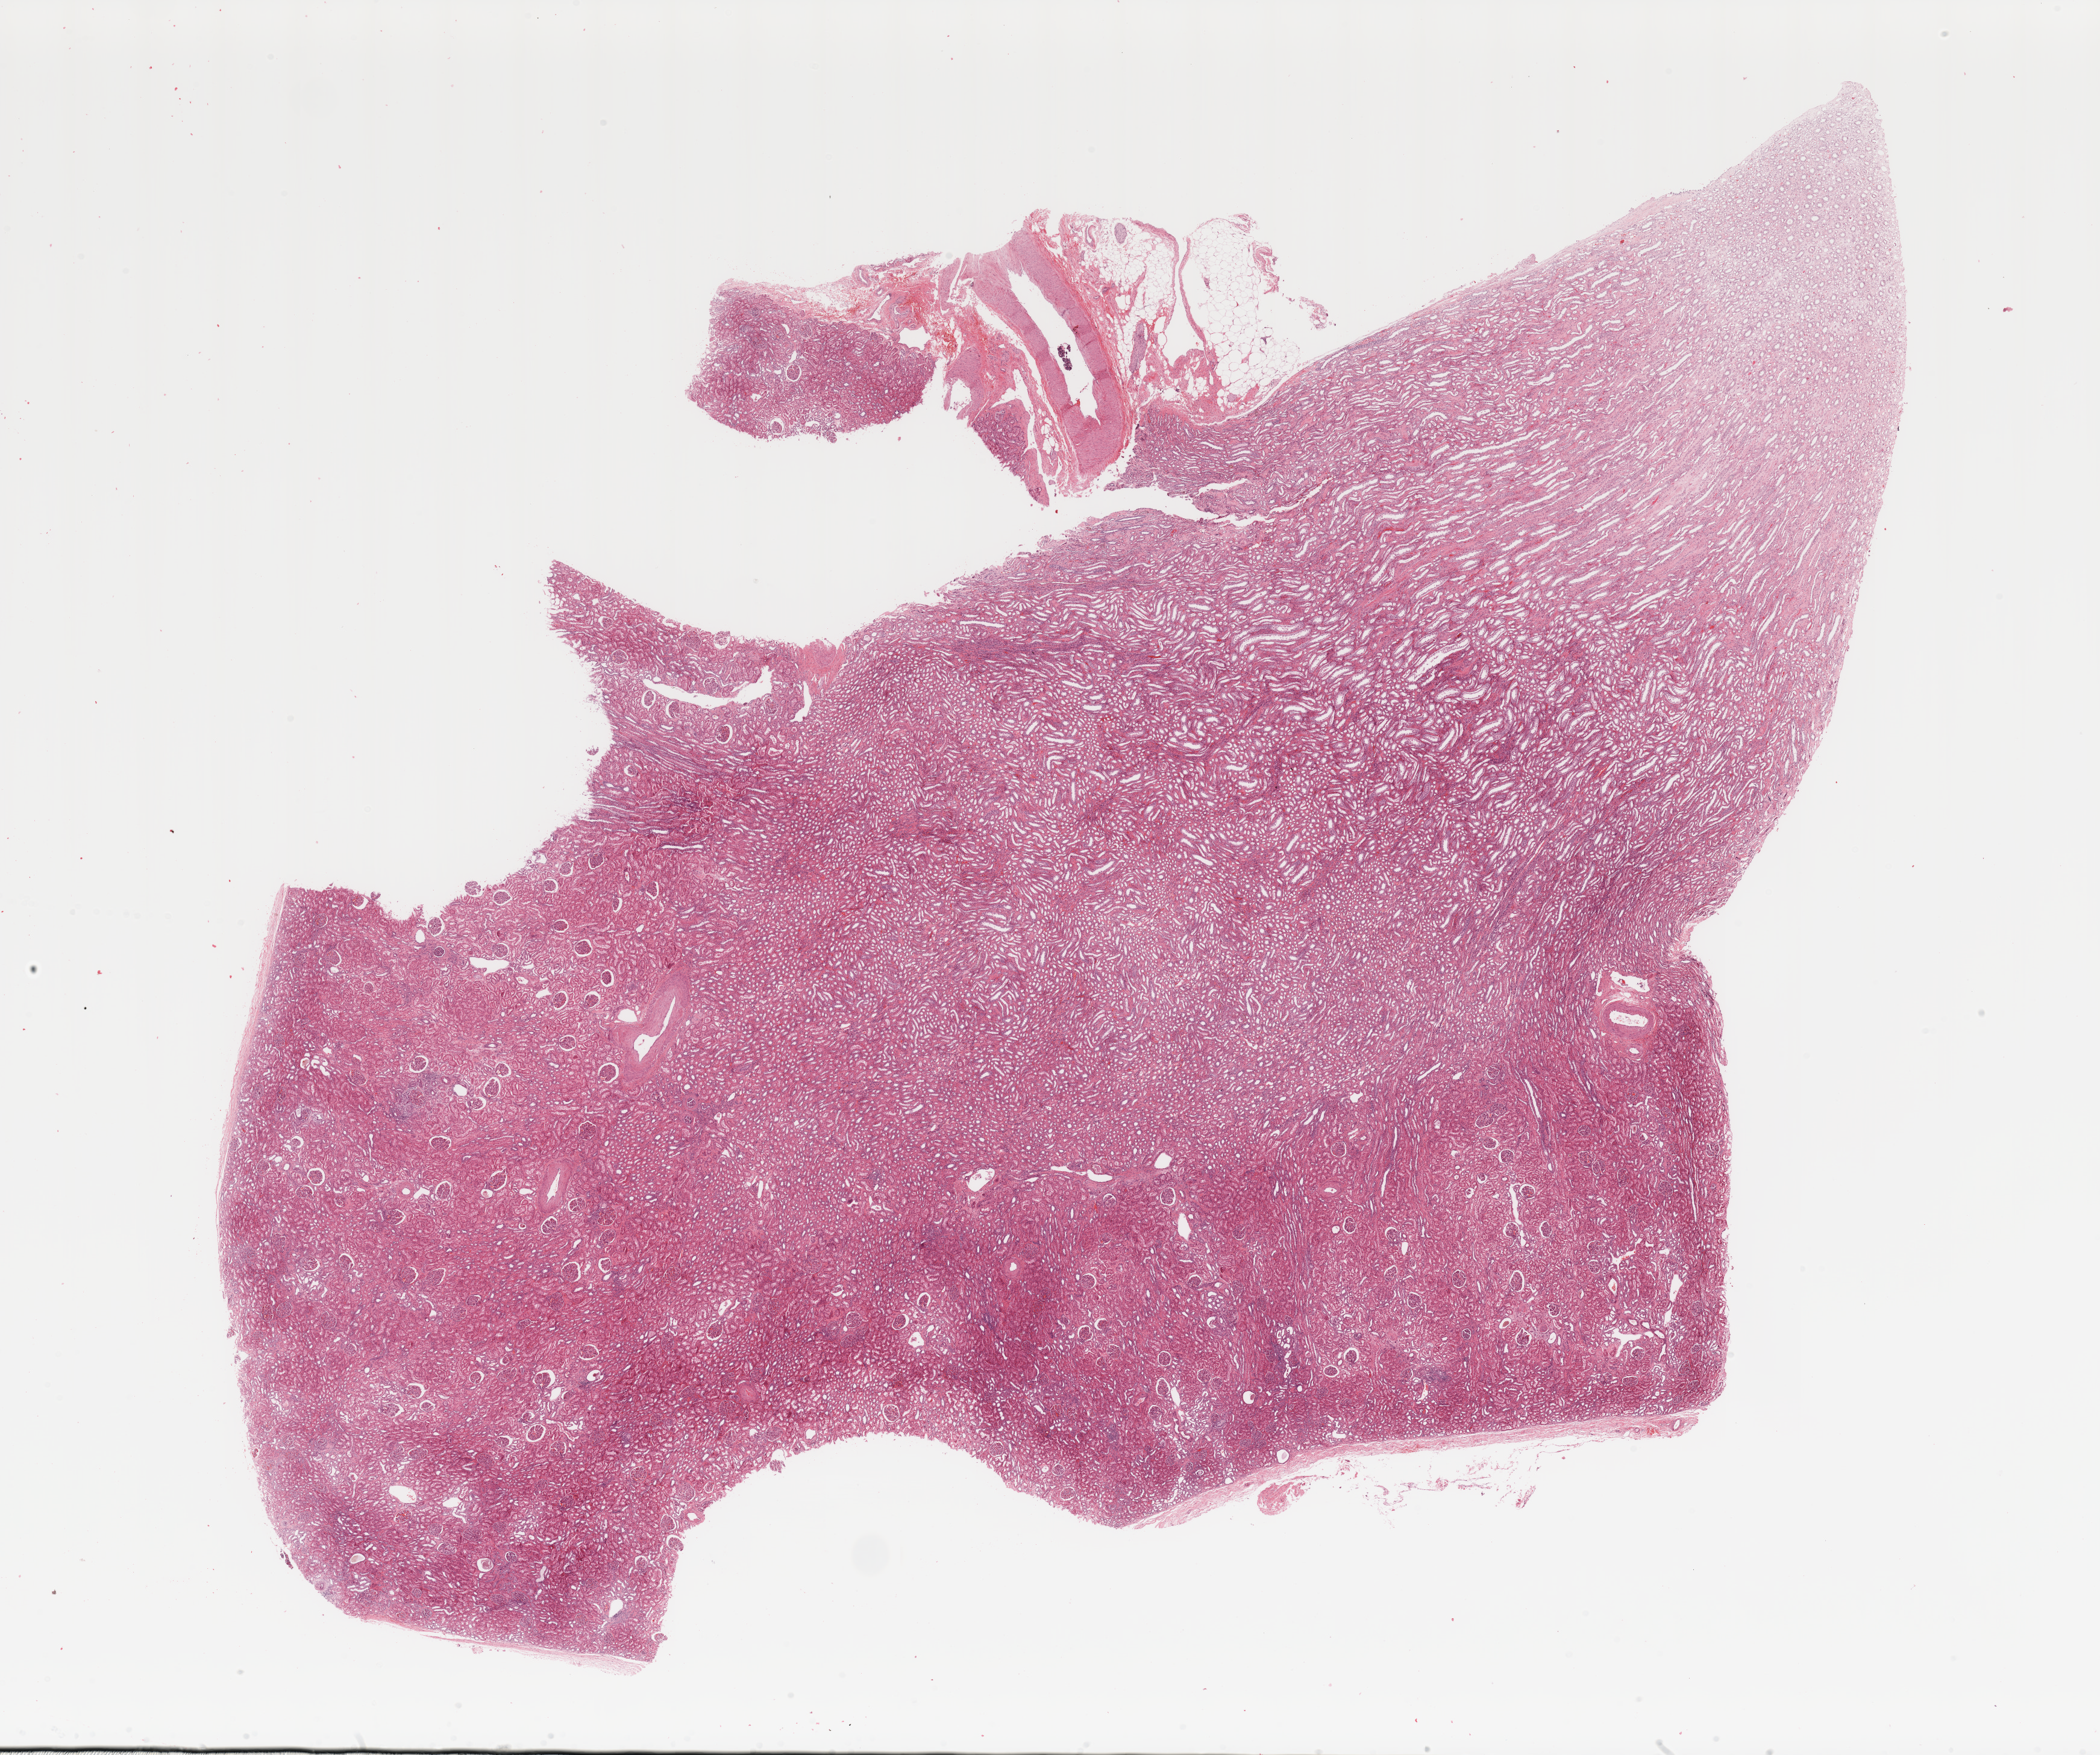
Whole-slide histology image, H&E-stained — whole scanned area (about 27.6 x 23.0 mm, acquisition: 20x scan) shown as a low-resolution overview, normal (non-tumour) tissue sample, sampled site: kidney. Patient: female, age 57 years.
This section: normal (non-tumour) tissue from the same patient. Patient diagnosis: Renal cell carcinoma, NOS.